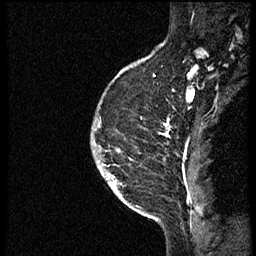
Breast MRI (dynamic contrast-enhanced), one sagittal slice; slice 45 of 56 in the series (ordered by position); dynamic contrast-enhanced study with each time point stored as its own series, time point 2 of 3 at this slice position (early post-contrast, ordered by acquisition time); 1.5 T; TE 4.2 ms, TR 21.3 ms; 2 mm slice thickness; 256 × 256 image matrix. Patient: female, 41 years. Case-level facts recorded for this patient, not image findings: setting: breast cancer imaged before/during neoadjuvant chemotherapy; receptor status: HER2-positive.
Structures marked on this image (semi-automatic segmentation, software-assisted and operator-edited):
- analysis volume of interest (the breast-tissue region the enhancement analysis was run in; not a lesion): bounding box (x1, y1, x2, y2) in pixels: (104, 73, 176, 205)
- tumour enhancement mask (voxels above the 100 % enhancement threshold inside the analysis volume of interest): (106, 122, 170, 180)